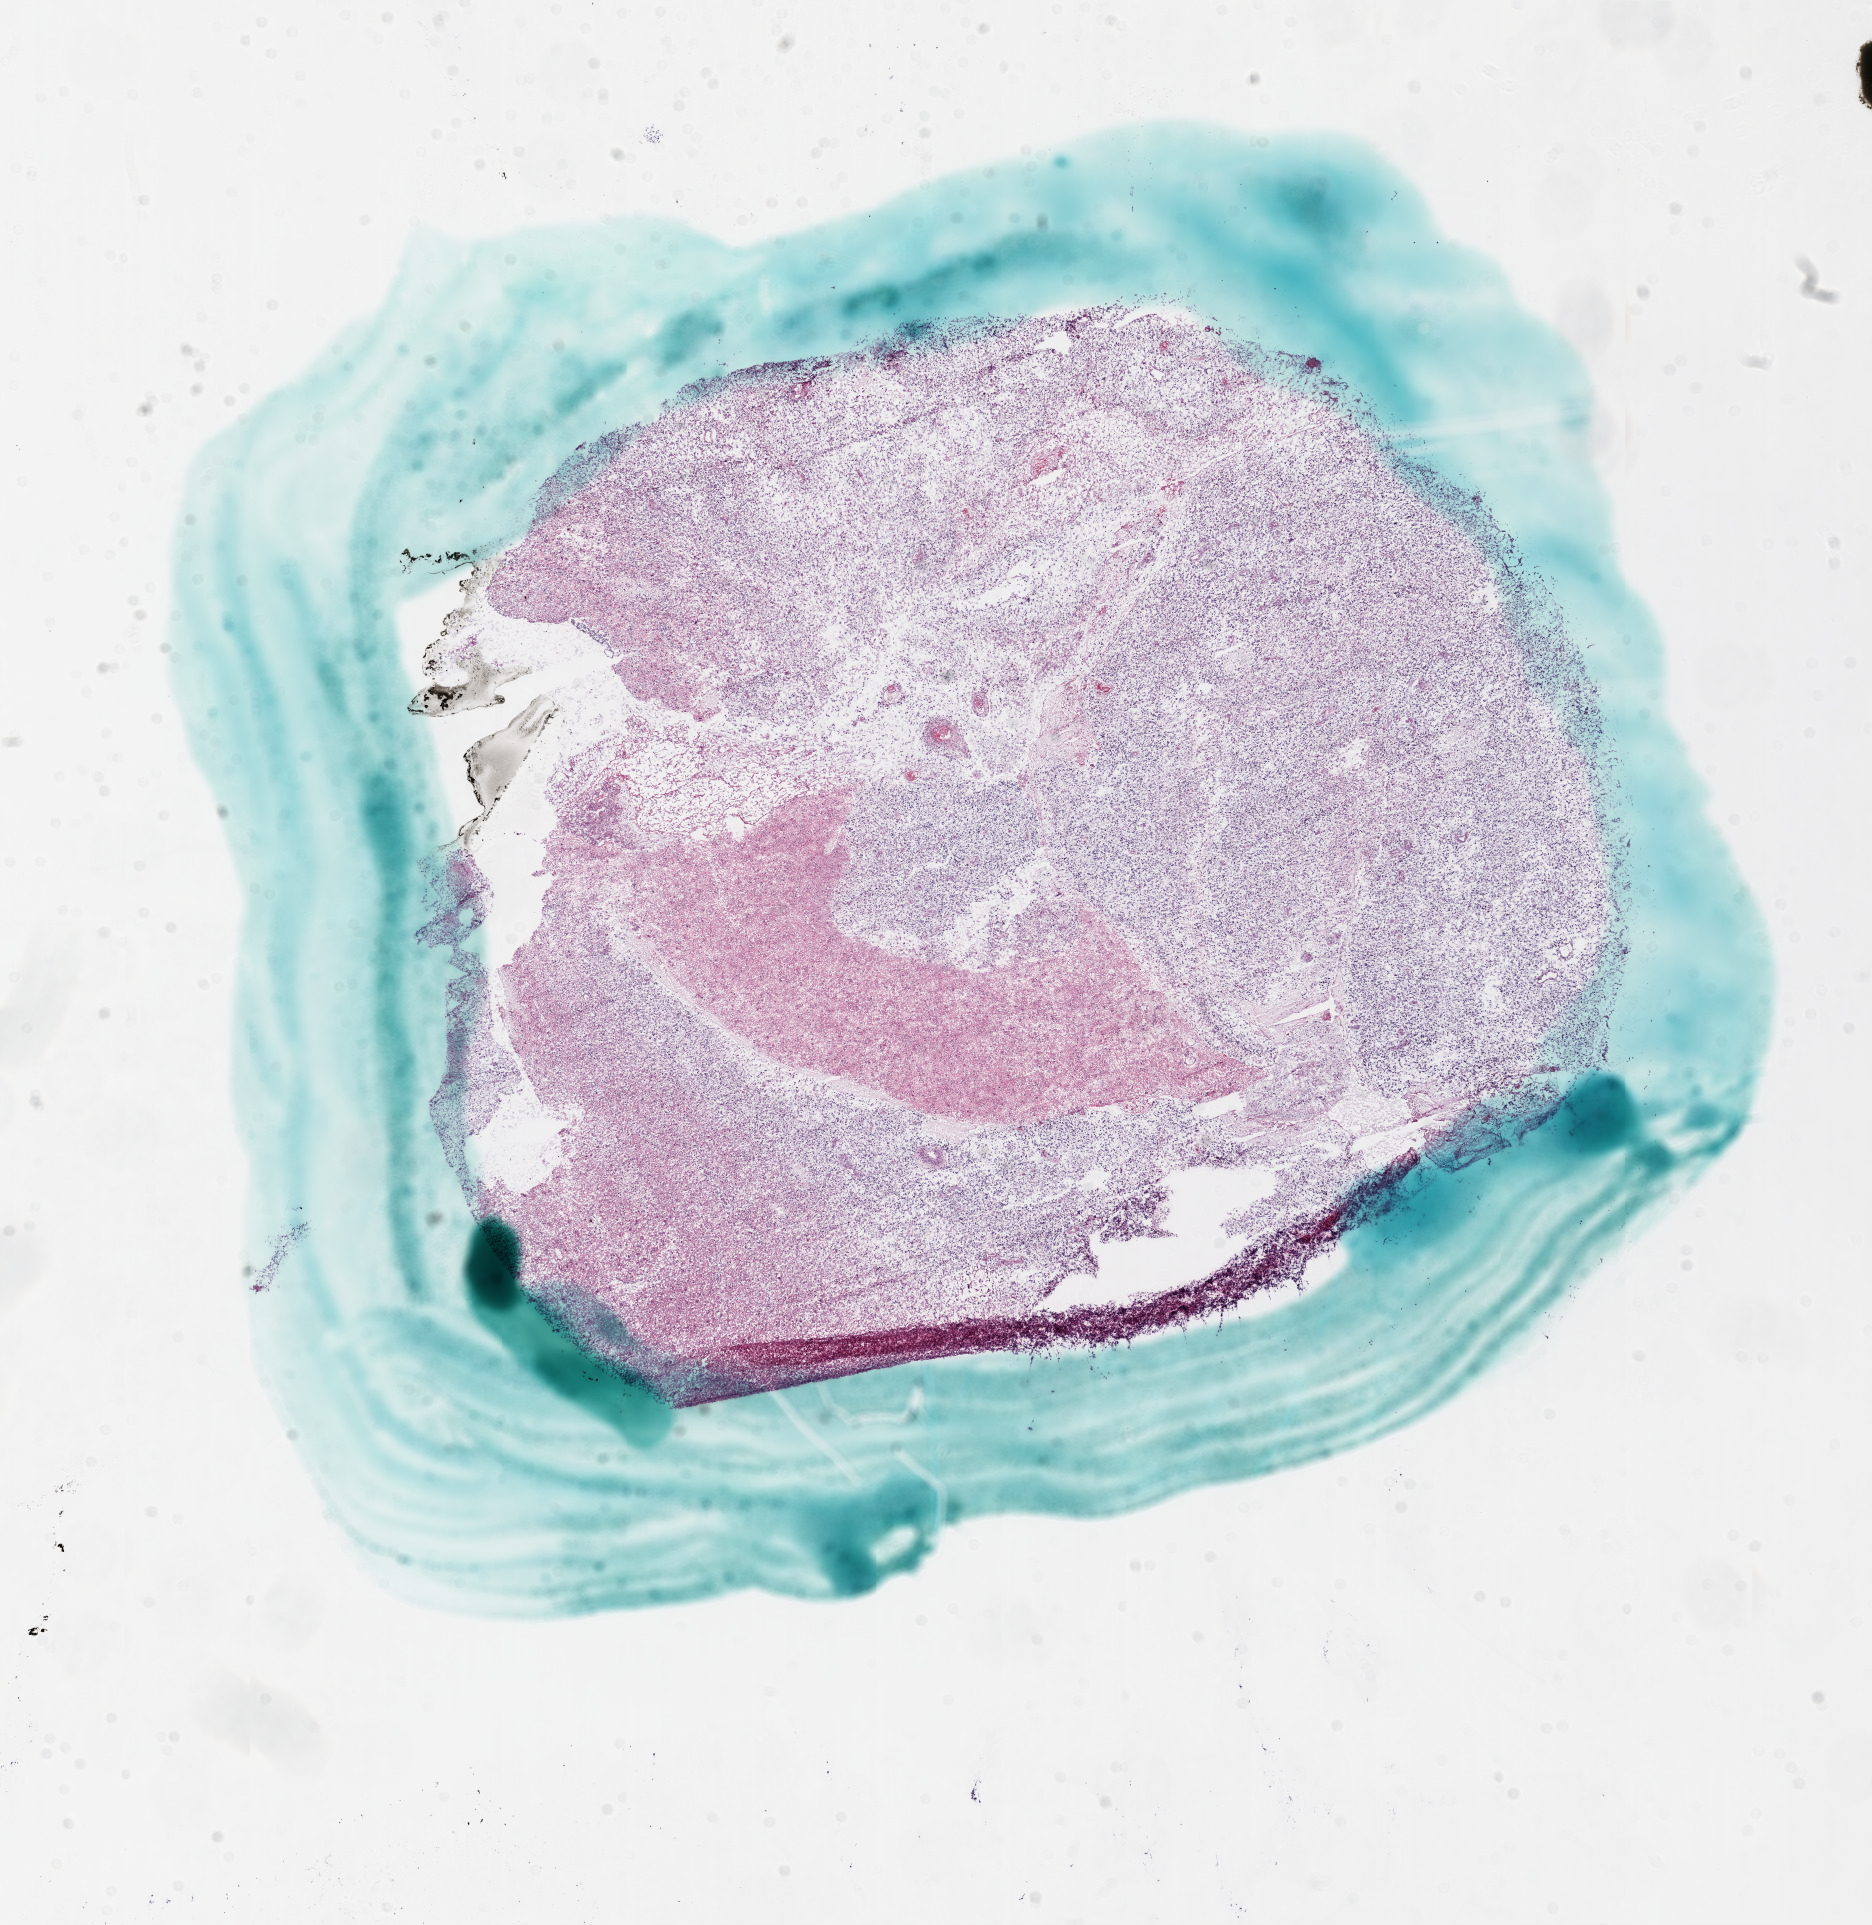
Whole-slide histology image, Hematoxylin and eosin (H&E) stained — a low-resolution overview of the entire scanned area, about 15.0 x 15.4 mm; frozen section from the bottom of the tissue portion; sample: primary tumour, brain. Male patient; age at initial diagnosis 51 years. Composition of this section per pathologist review: tumour cells 75%, tumour nuclei 95%, normal cells 0%, stromal cells 15%, necrosis 10%.
• pathologic diagnosis: Glioblastoma